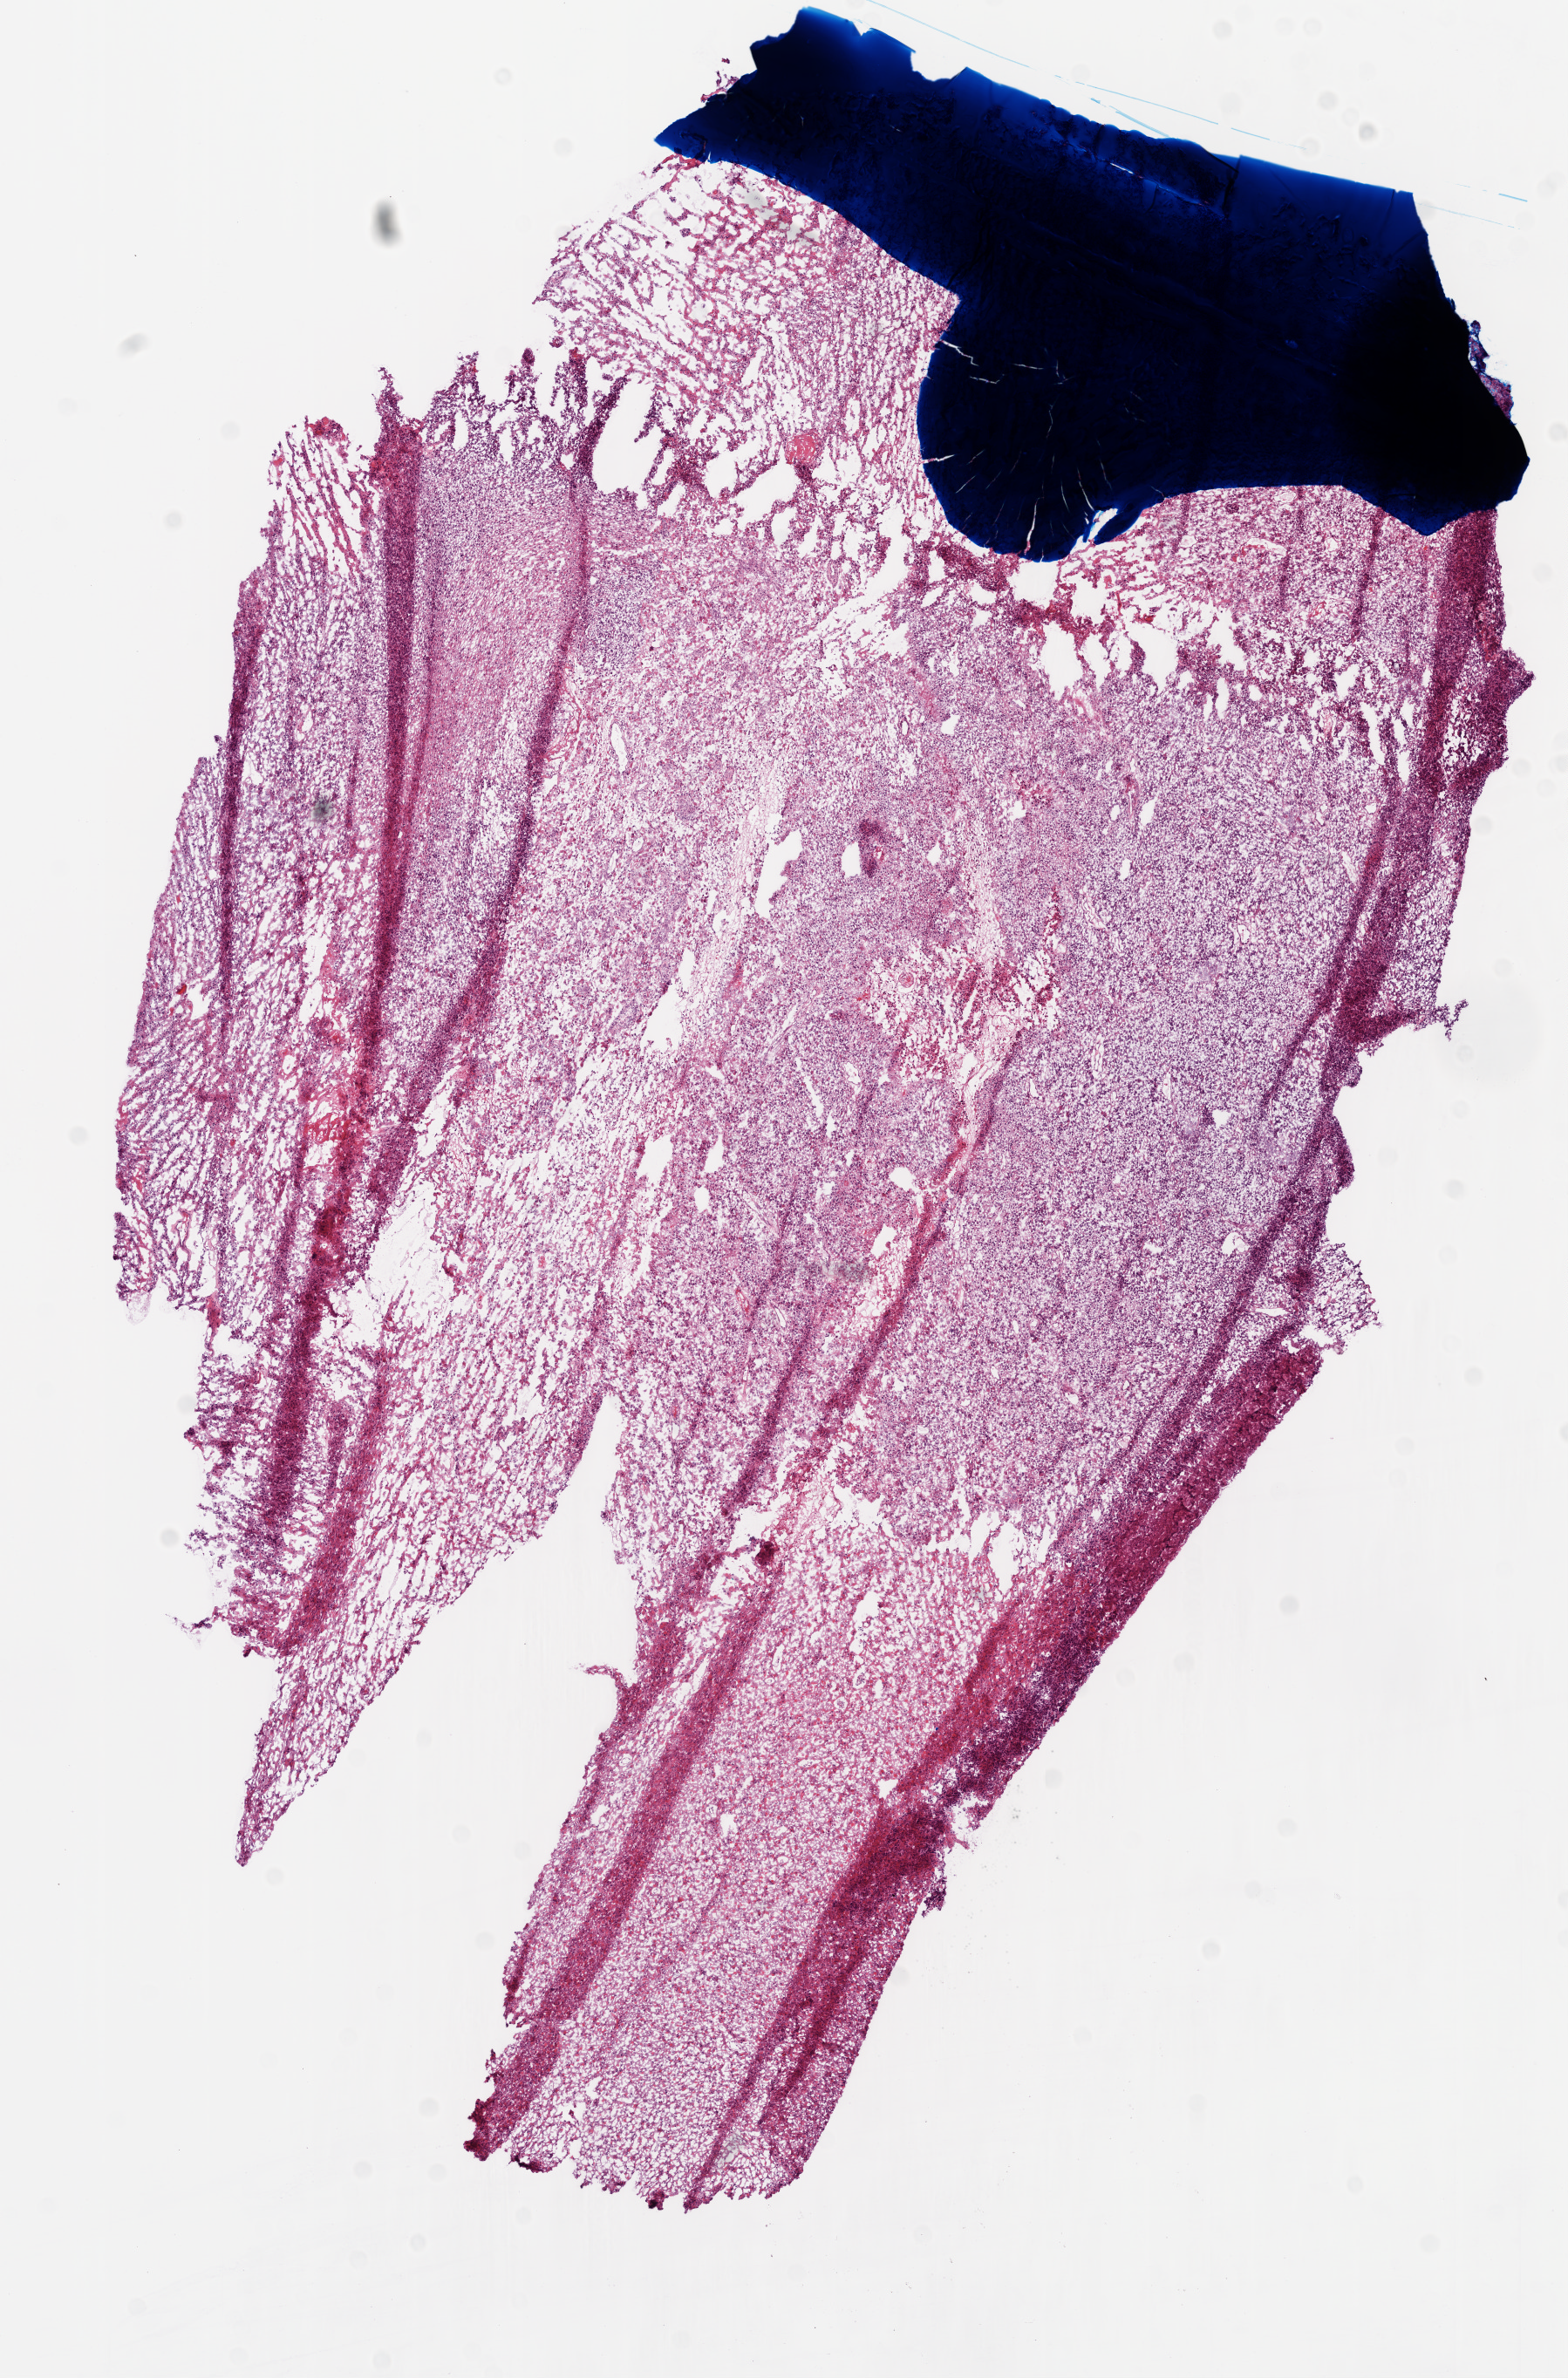
Whole-slide histology image, Hematoxylin and eosin (H&E) stained — low-resolution overview of the scanned area, about 7.3 x 11.0 mm. Frozen section from the top of the tissue portion. Brain, primary tumour sample. Female, age 61 years at initial diagnosis. Composition of this section per pathologist review: tumour cells 80%, tumour nuclei 90%, normal cells 0%, stromal cells 0%, necrosis 20%. Infiltration values recorded for this section: lymphocyte infiltration 100%.
Diagnosis: Glioblastoma.